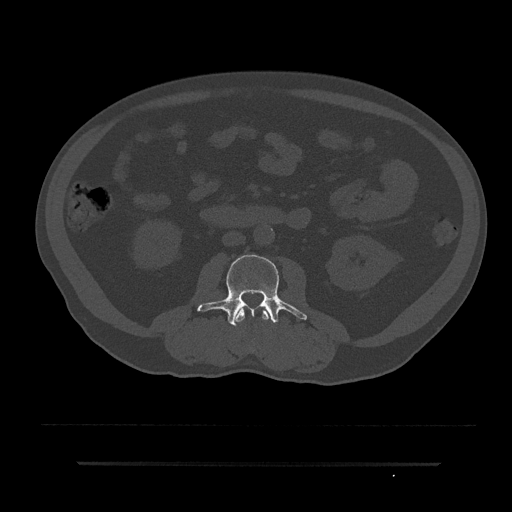
CT including the spine, one axial slice; position 19 of 797 along the scan axis; reconstruction kernel Br40s/3; bone window (W 1800 / L 400 HU); 512 × 512 image matrix, field of view 464 × 464 mm. Patient: male, 59 years. Case-level facts recorded for this patient, not image findings: primary cancer: bile ducts; vertebrae with lytic lesions (as recorded): T10.
Outlined on this slice (semi-automatically segmented with operator editing):
- L2 vertebra: bounding box <234,307,269,323> (left, top, right, bottom; pixels)
- L3 vertebra: <197,254,307,326>